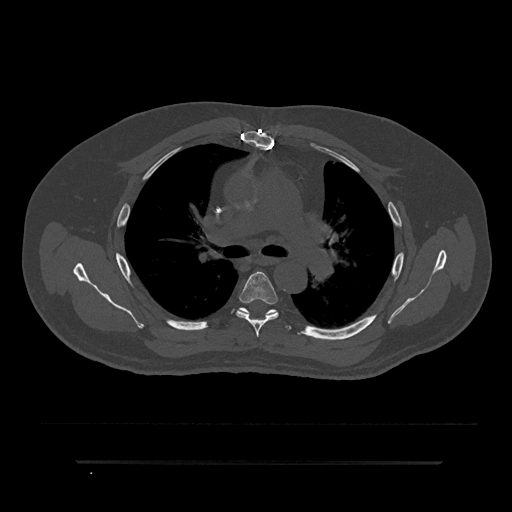
CT including the spine, one axial slice. Position 563 of 797 along the scan axis. Reconstruction kernel Br40s/3. 120 kVp. Bone window (W 1800 / L 400 HU). 0.5 mm slice thickness. 512 × 512 image matrix, field of view 464 × 464 mm. Male patient, age 59 years. From the clinical record (not read from this slice): primary cancer: bile ducts; vertebrae with lytic lesions (as recorded): T10.
Annotated regions visible in this slice (semi-automatically segmented with operator editing):
- T5 vertebra: bounding box (x1, y1, x2, y2) in pixels: (236, 271, 279, 337)
- T6 vertebra: (239, 308, 291, 331)